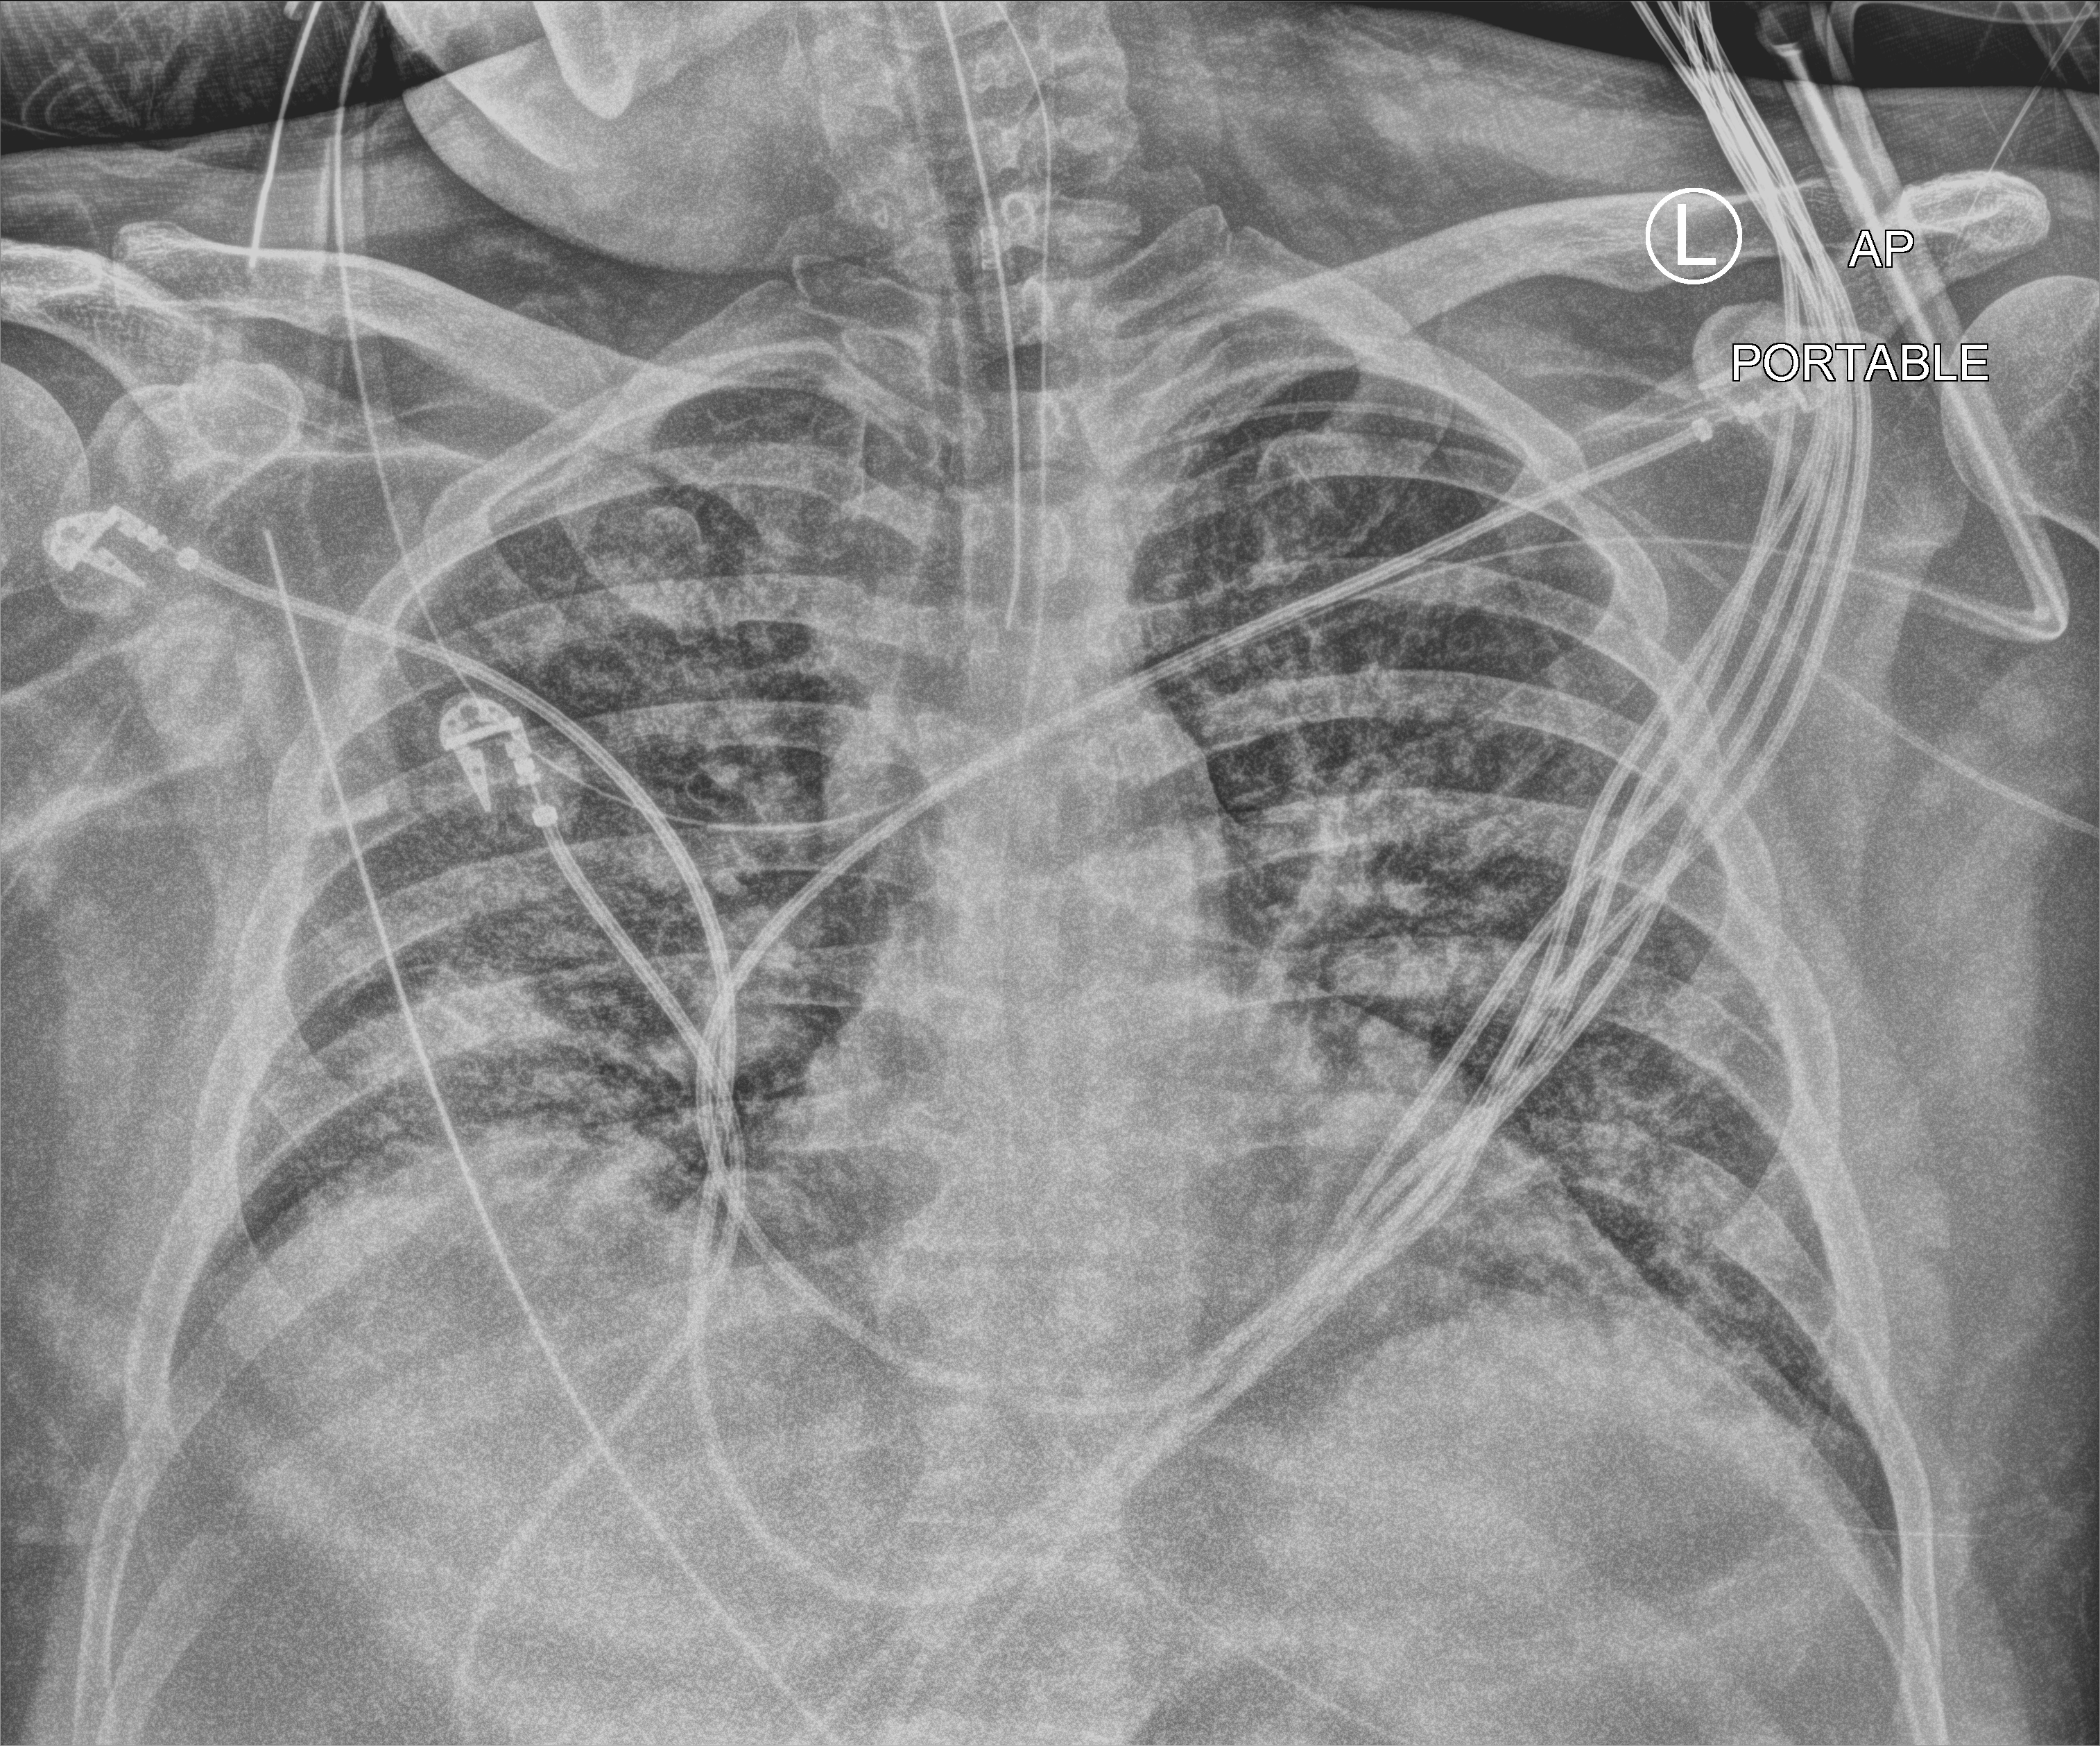
Chest X-ray (portable); anteroposterior (AP) projection. Male patient hospitalised with COVID-19, age 18–59 years.
Admission-level facts for this patient (not findings on this image; timing relative to this image not recorded):
- COPD (admission record): no
- diabetes (admission record): no